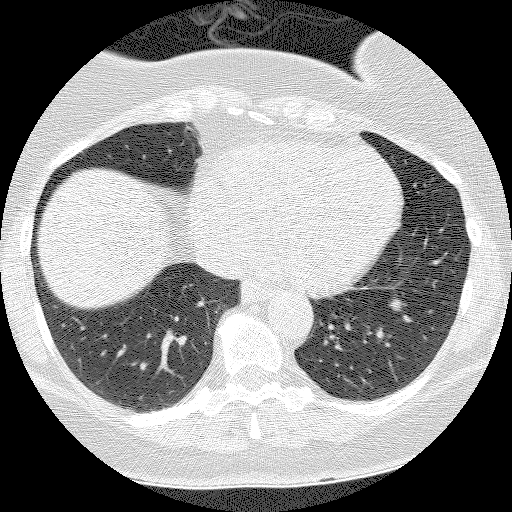
Axial slice from a low-dose chest CT screening exam. Baseline annual screen. Lung window (W 1500 / L -600 HU). 2.5 mm slice thickness. Lung (sharp) reconstruction kernel (BONE). Slice 94 of 135 in the series. 512 × 512 image matrix, field of view 300 × 300 mm. Female, age 55 years at enrolment. Former smoker at enrolment.
• Expert reader's lesion annotation, bounding box [x1, y1, x2, y2] px = [371, 285, 422, 332].
• The screening reader recorded 3 non-calcified nodules or masses ≥4 mm on this exam (left lower lobe, right lower lobe, right lower lobe); which of them this box marks is not recorded.
• Official screen result: positive, change unspecified: nodule(s) >= 4 mm or enlarging nodule(s), mass(es), or other non-specific abnormalities suspicious for lung cancer.
• Participant outcome: lung cancer diagnosed 1026 days after this screen — carcinoid tumor, NOS, left lower lobe, carcinoid, stage not assessed, 10 mm at pathology.